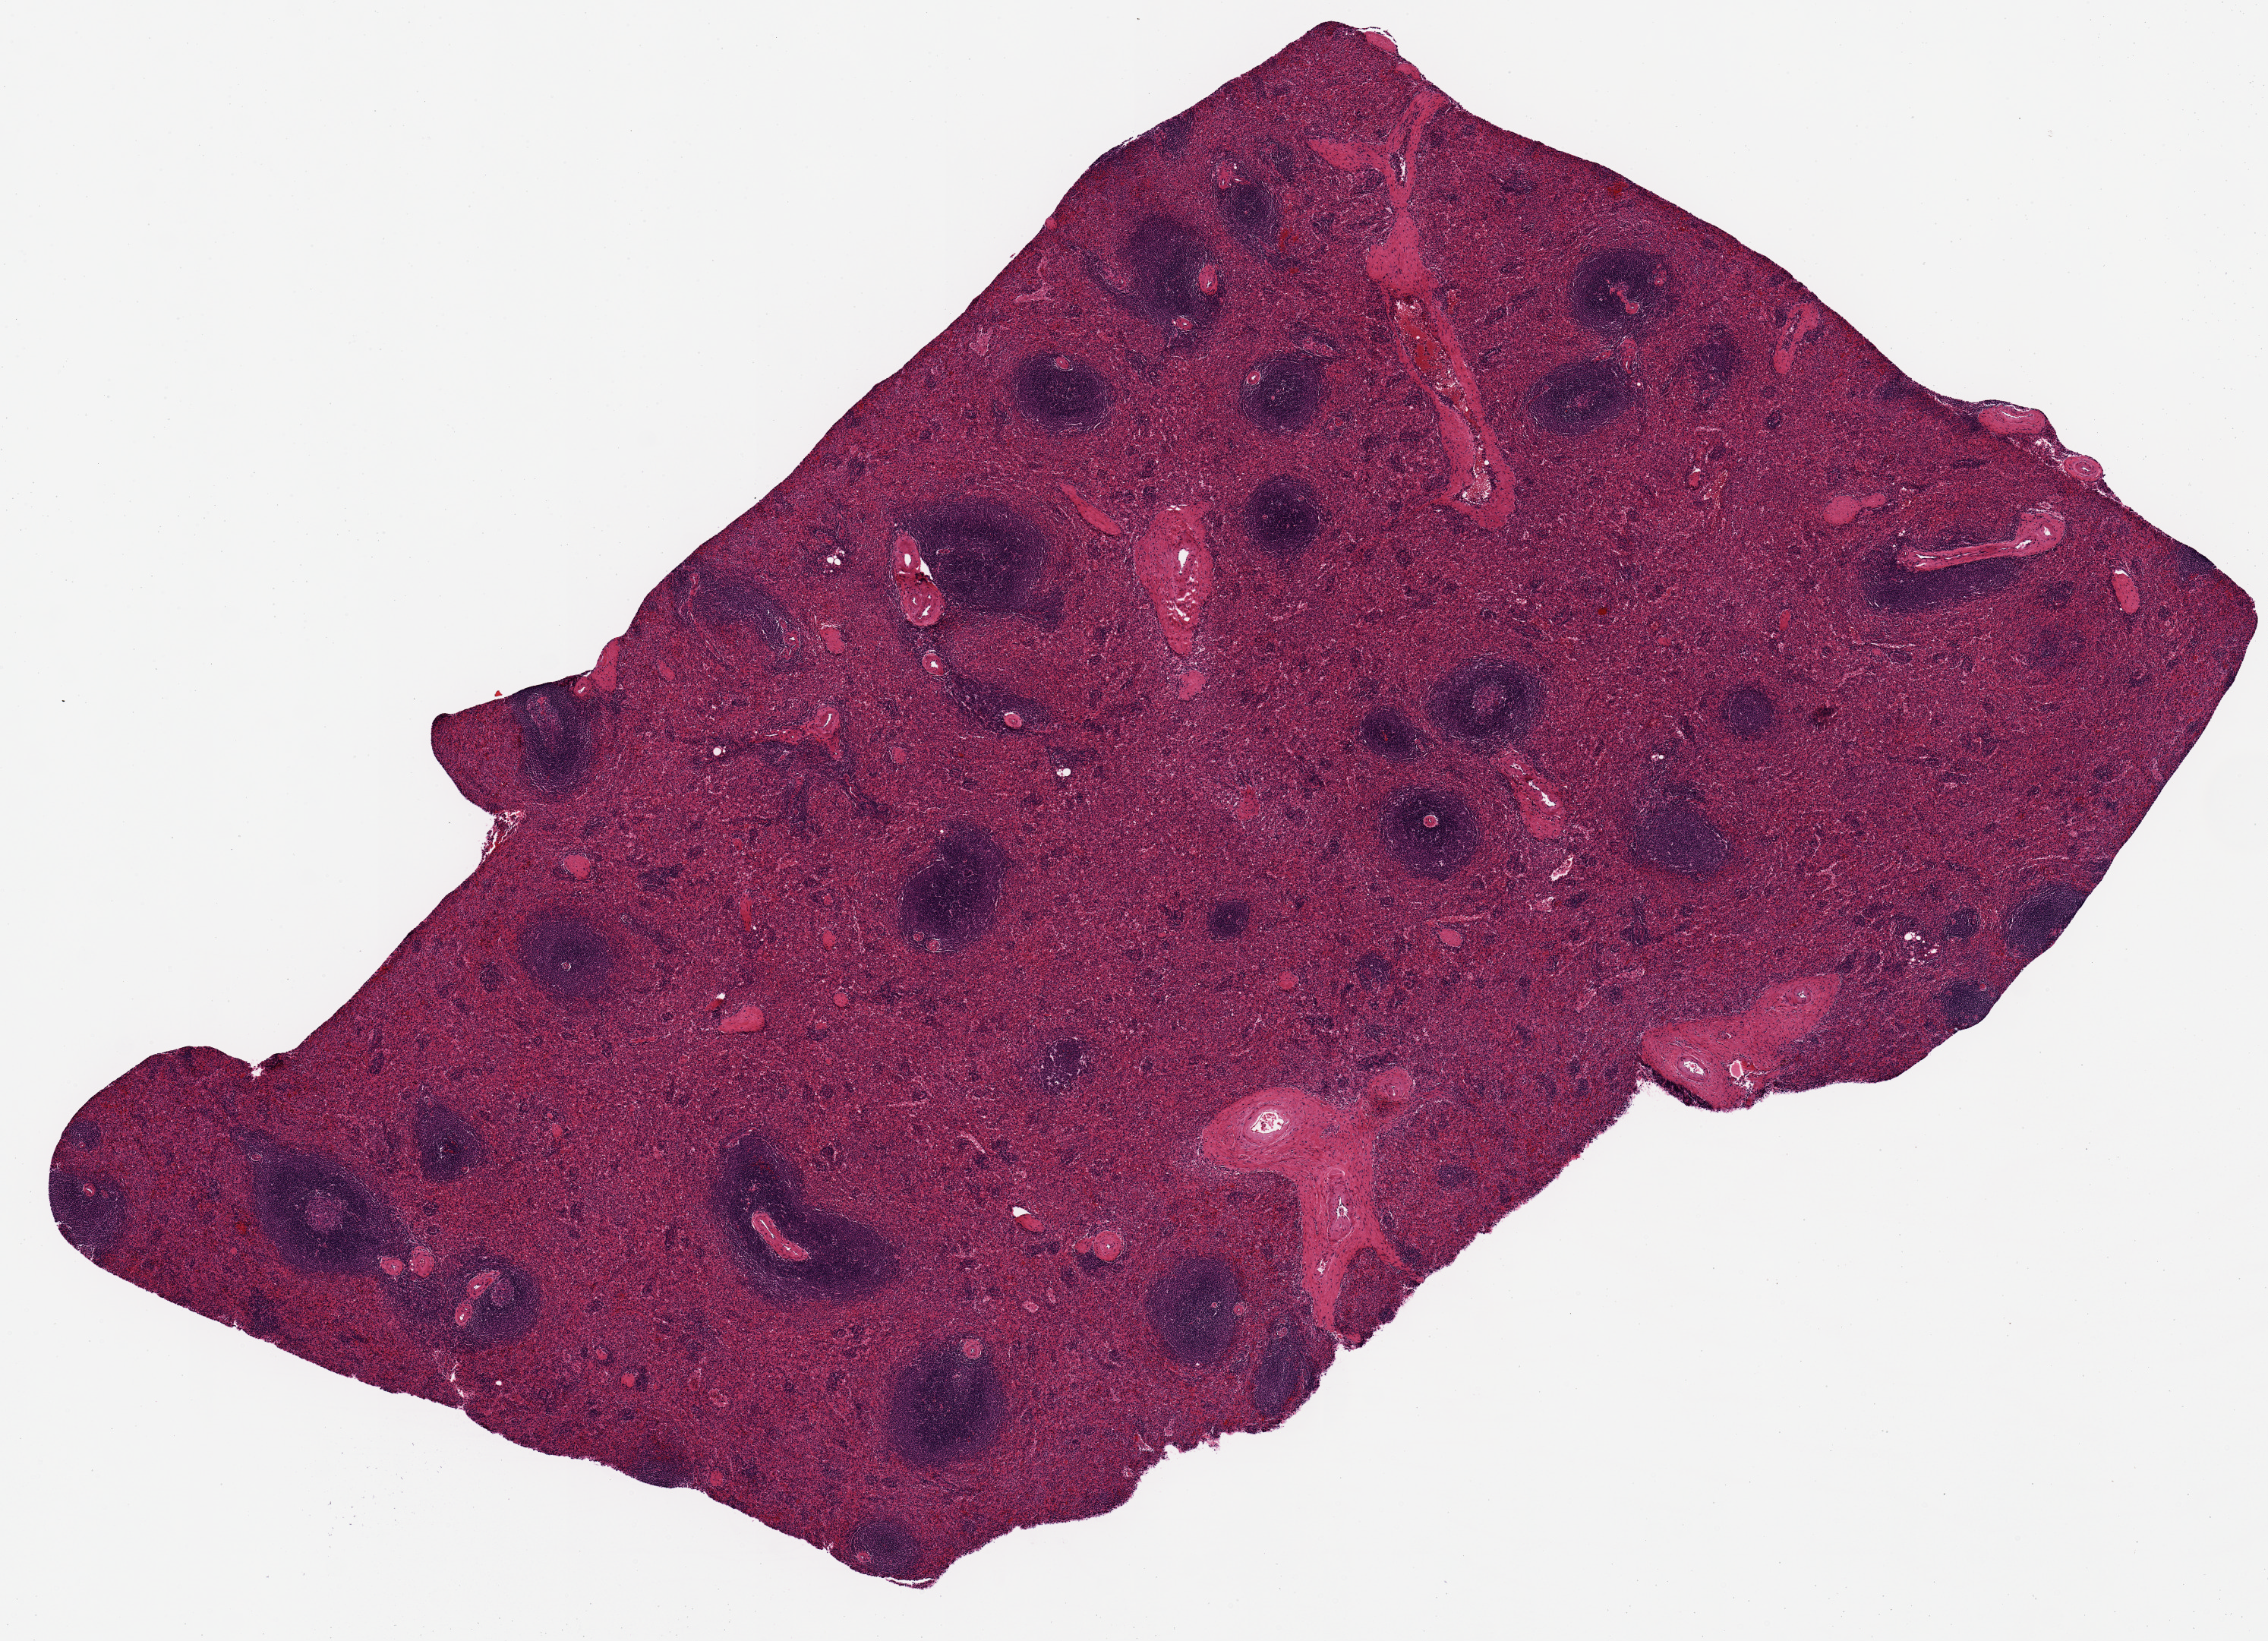
H&E whole-slide image, brightfield, a low-resolution overview of the entire scanned area, about 11.8 x 8.5 mm. PAXgene-fixed, paraffin-embedded tissue. Target tissue: spleen. Donor tissue sample. Female donor.
Pathologist's review note for this sample: 8x8 mm.